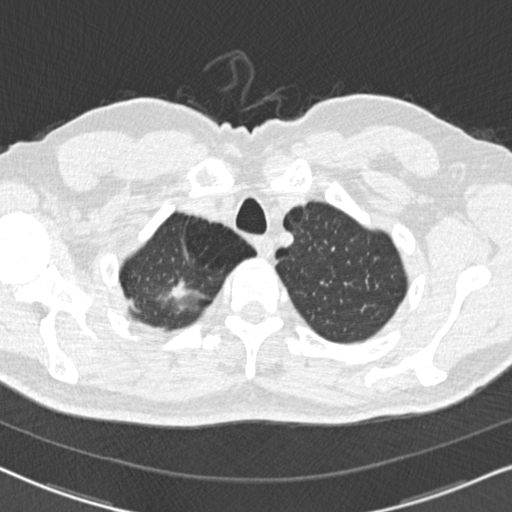
Chest CT (low-dose screening protocol), one axial image, baseline screening round, lung window (W 1500 / L -600 HU), 2 mm slice thickness. Male, age 56 years at enrolment. Former smoker at enrolment.
Lesion marked by an expert reader, box from (x=145, y=270) to (x=200, y=313) px. No non-calcified nodule or mass ≥4 mm was recorded by the screening reader at this exam.